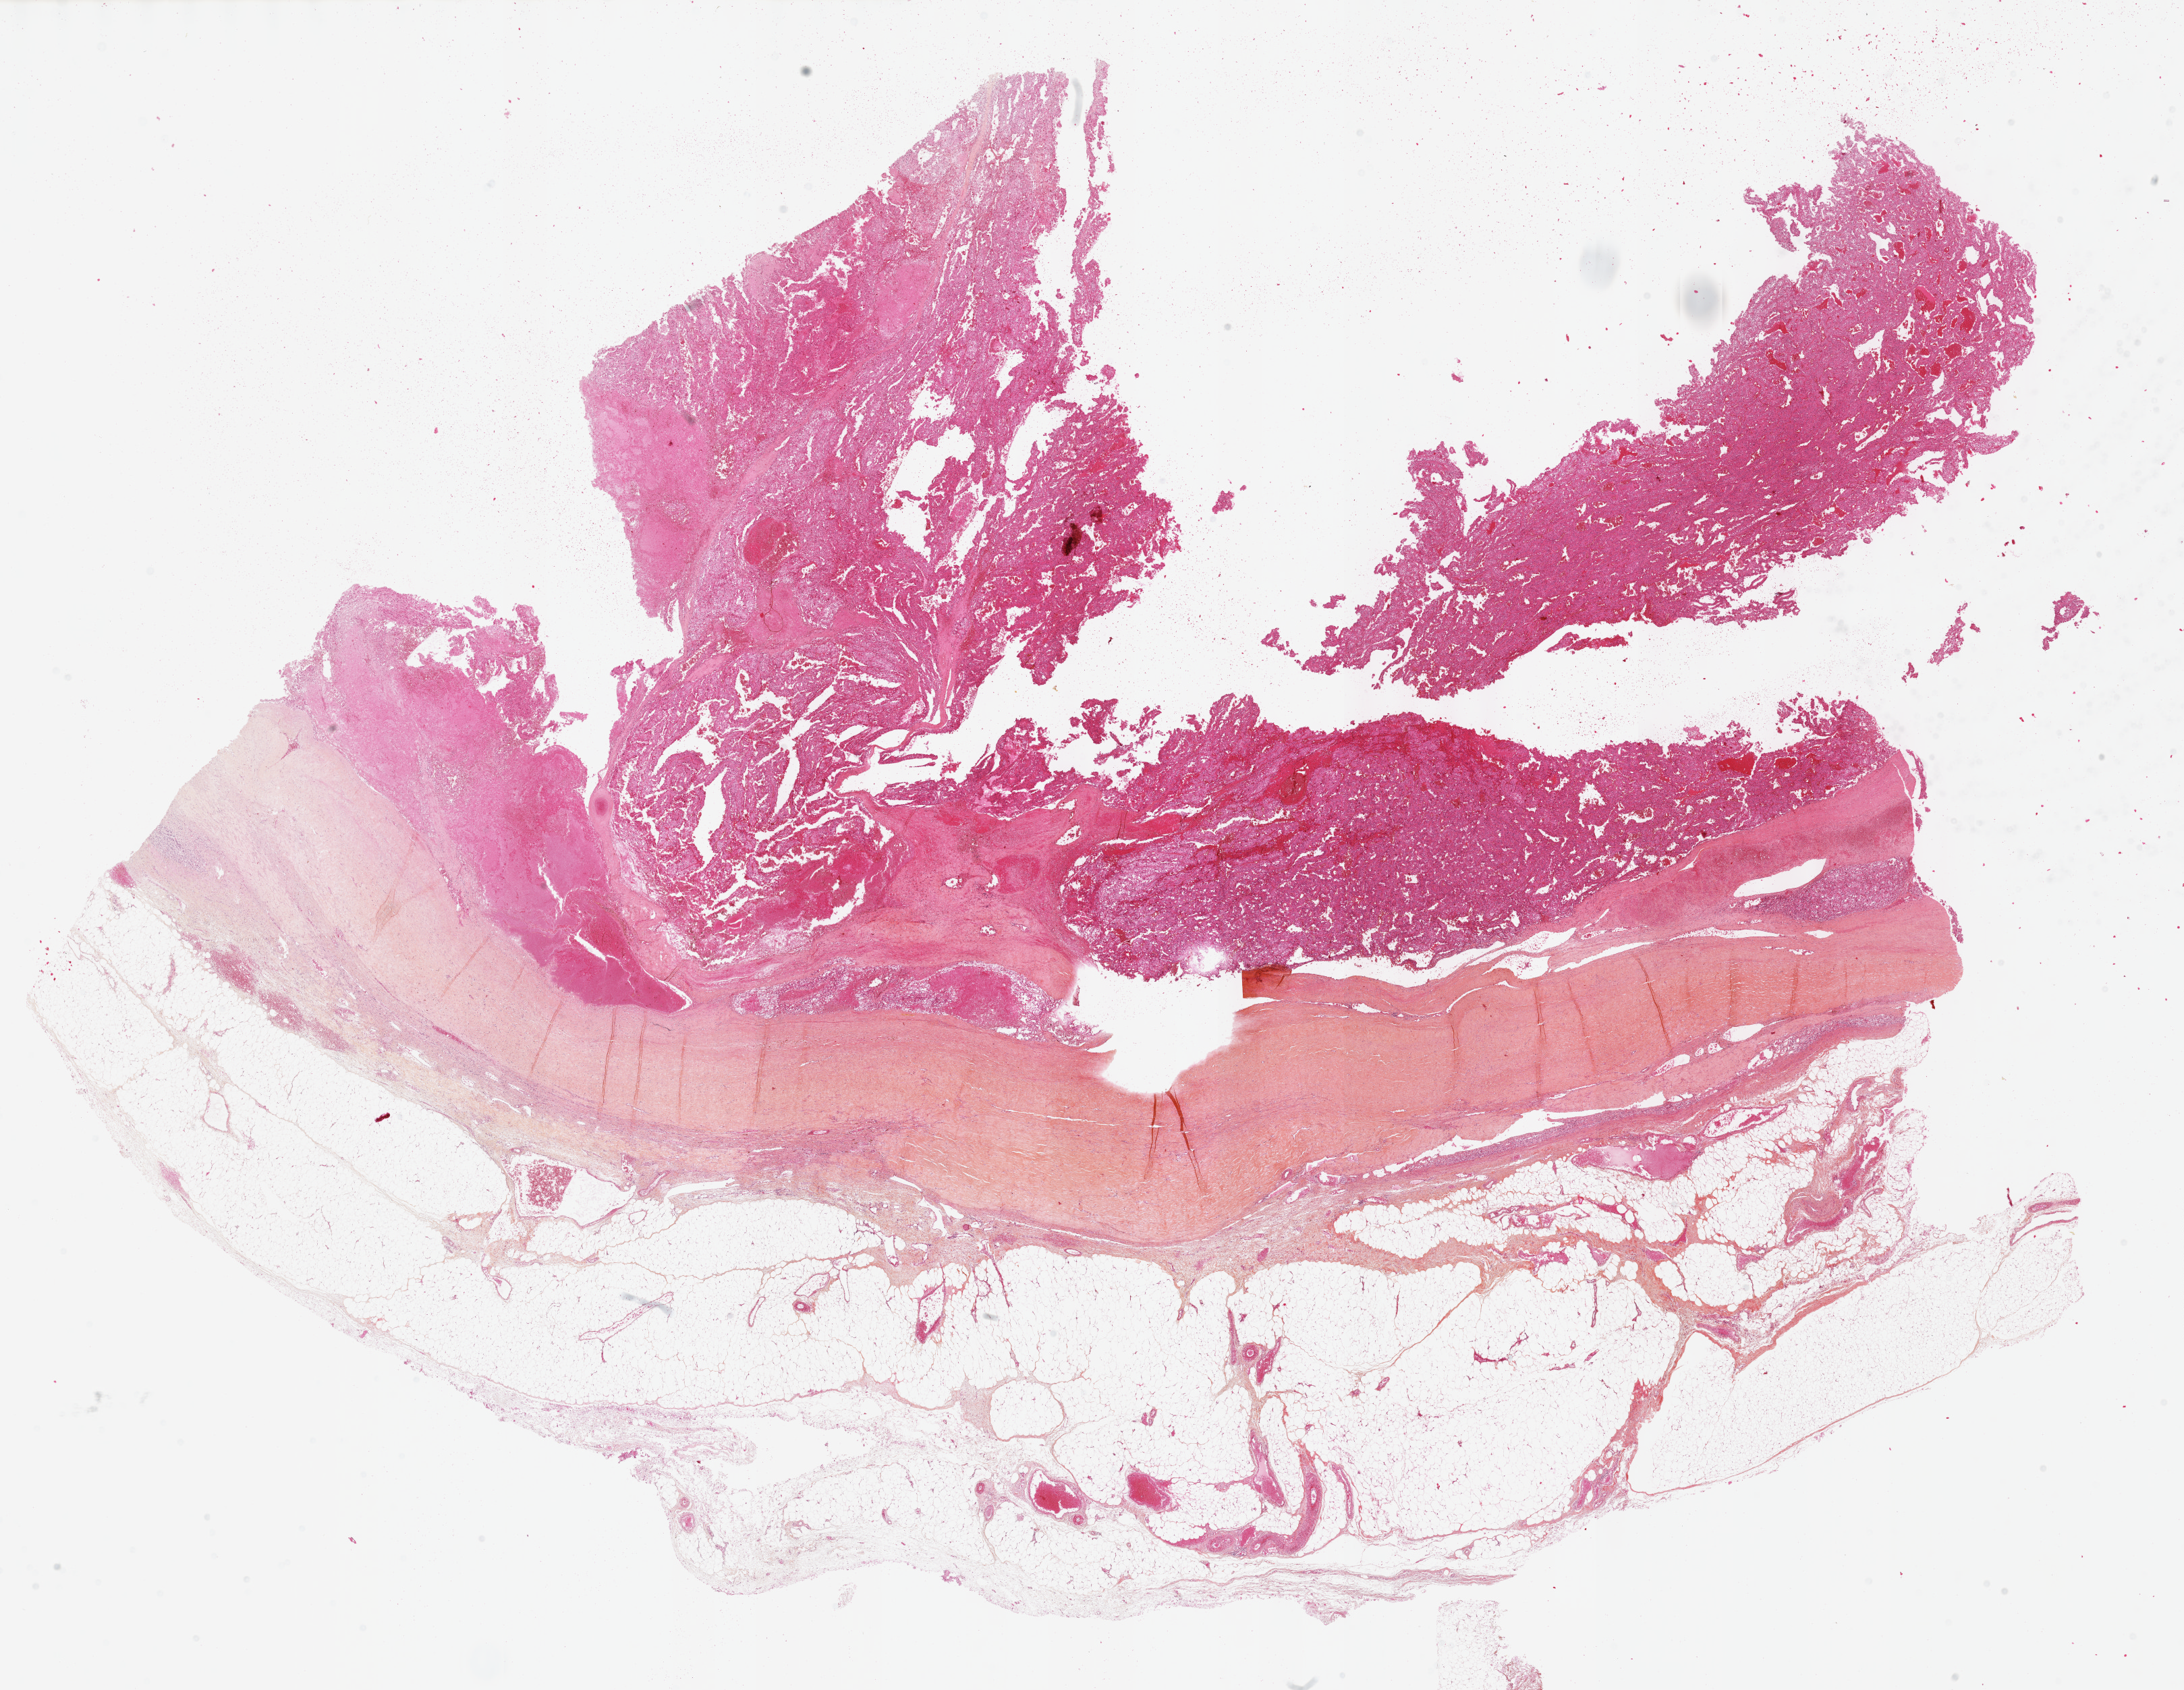
Hematoxylin and eosin (H&E) stained whole-slide image — a low-resolution overview of the entire scanned area, about 26.2 x 20.2 mm; FFPE section; adrenal cortex, primary tumour sample. Female, age 34 years at initial diagnosis.
Diagnosis: Adrenal cortical carcinoma (cortex of adrenal gland).